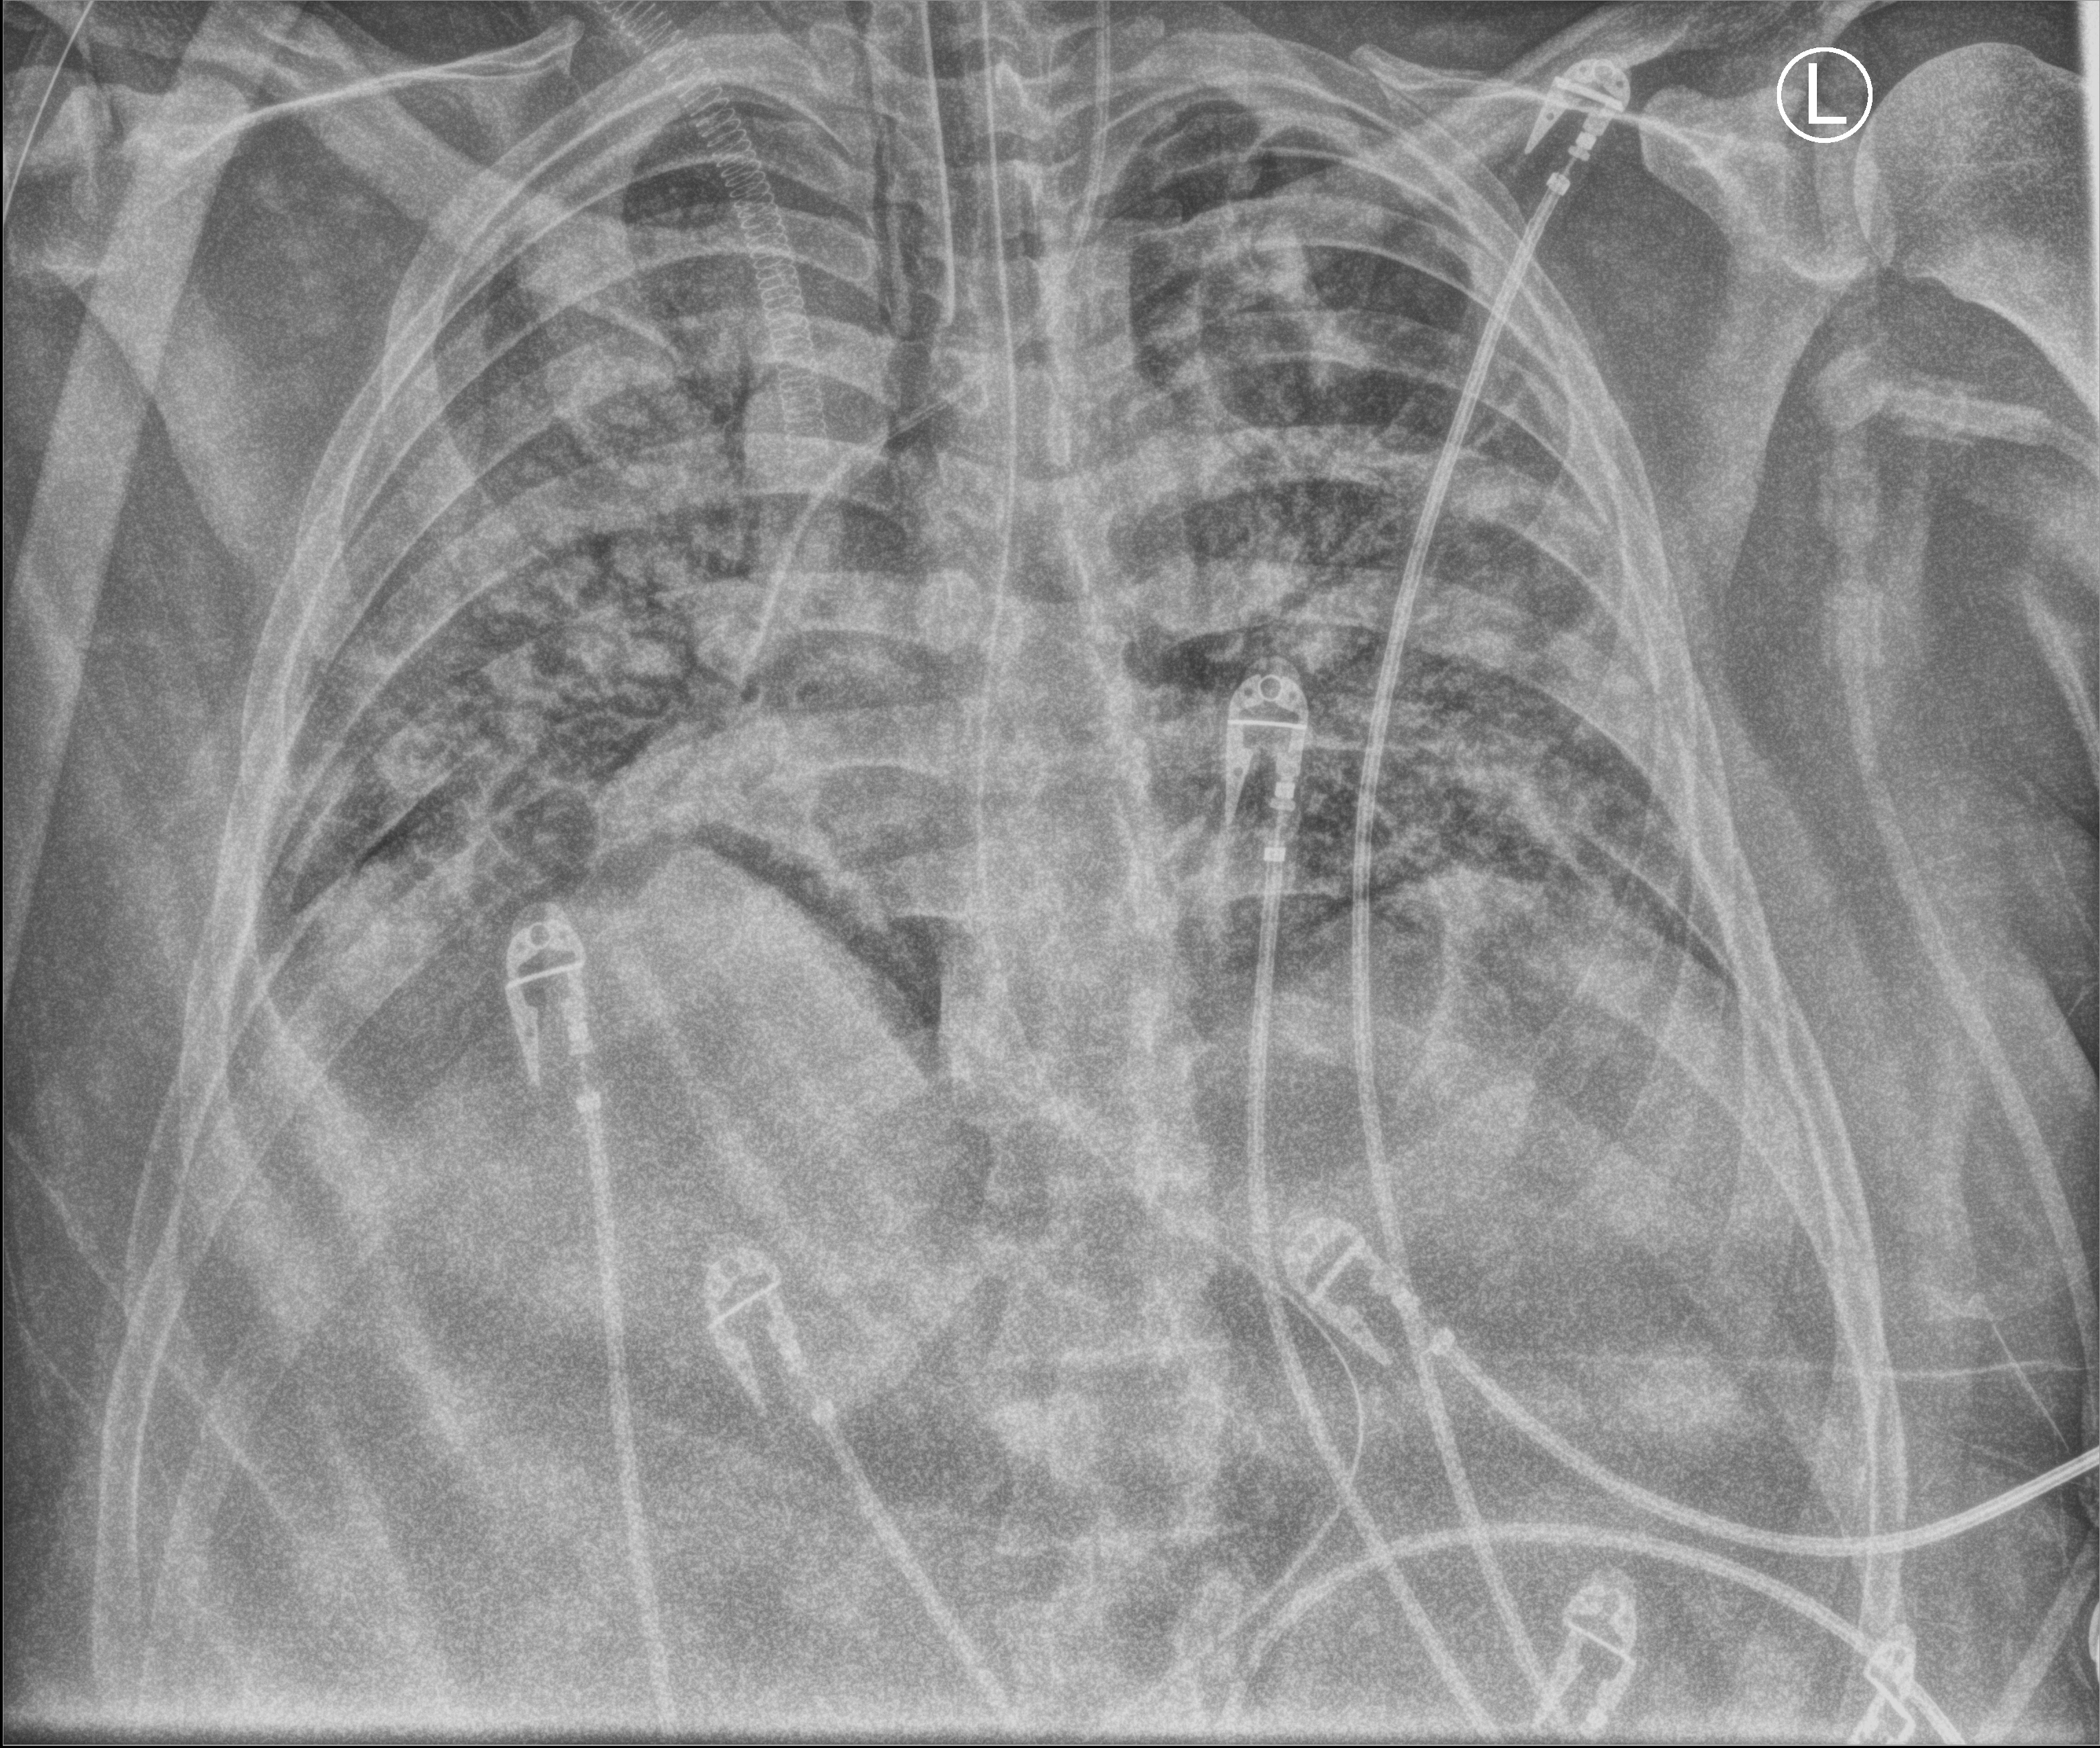
Chest X-ray (portable), anteroposterior (AP) projection. Adult patient hospitalised with COVID-19, age 18–59 years.
Admission-level facts for this patient (not findings on this image; timing relative to this image not recorded):
- chronic kidney disease (admission record): no